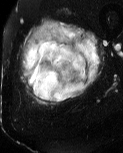
MRI of an extremity soft-tissue mass, one axial slice; slice 18 of 60 in the series (ordered by position); T2-weighted fat-saturated; MR volume resampled by the dataset authors to the PET/CT grid (not the native acquisition matrix); 3.27 mm slice thickness; 123 × 153 image matrix. Male patient. Case-level facts recorded for this patient, not image findings: histological type: pleiomorphic liposarcoma; grade: high; site of the primary tumour: left thigh.
Annotated regions visible in this slice (expert contour drawn on MRI and transferred to this co-registered scan by the dataset authors):
- gross tumour volume including surrounding oedema: bounding box [x1, y1, x2, y2] px = [20, 18, 105, 107]
- gross tumour volume (mass): [27, 40, 89, 101]